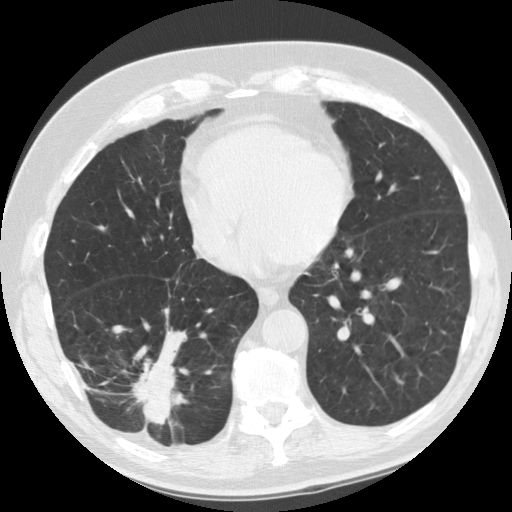
Low-dose screening chest CT, one axial slice. Slice 43 of 135 in the series (ordered by position). Reconstruction kernel STANDARD. 120 kVp. Lung window (W 1500 / L -600 HU). 2.5 mm slice thickness. 512 × 512 image matrix, field of view 340 × 340 mm.
Structures marked on this image (expert manual segmentation):
- lesion 1 (tumor, lower lobe of right lung): bounding box (x1, y1, x2, y2) in pixels: (130, 358, 183, 425)